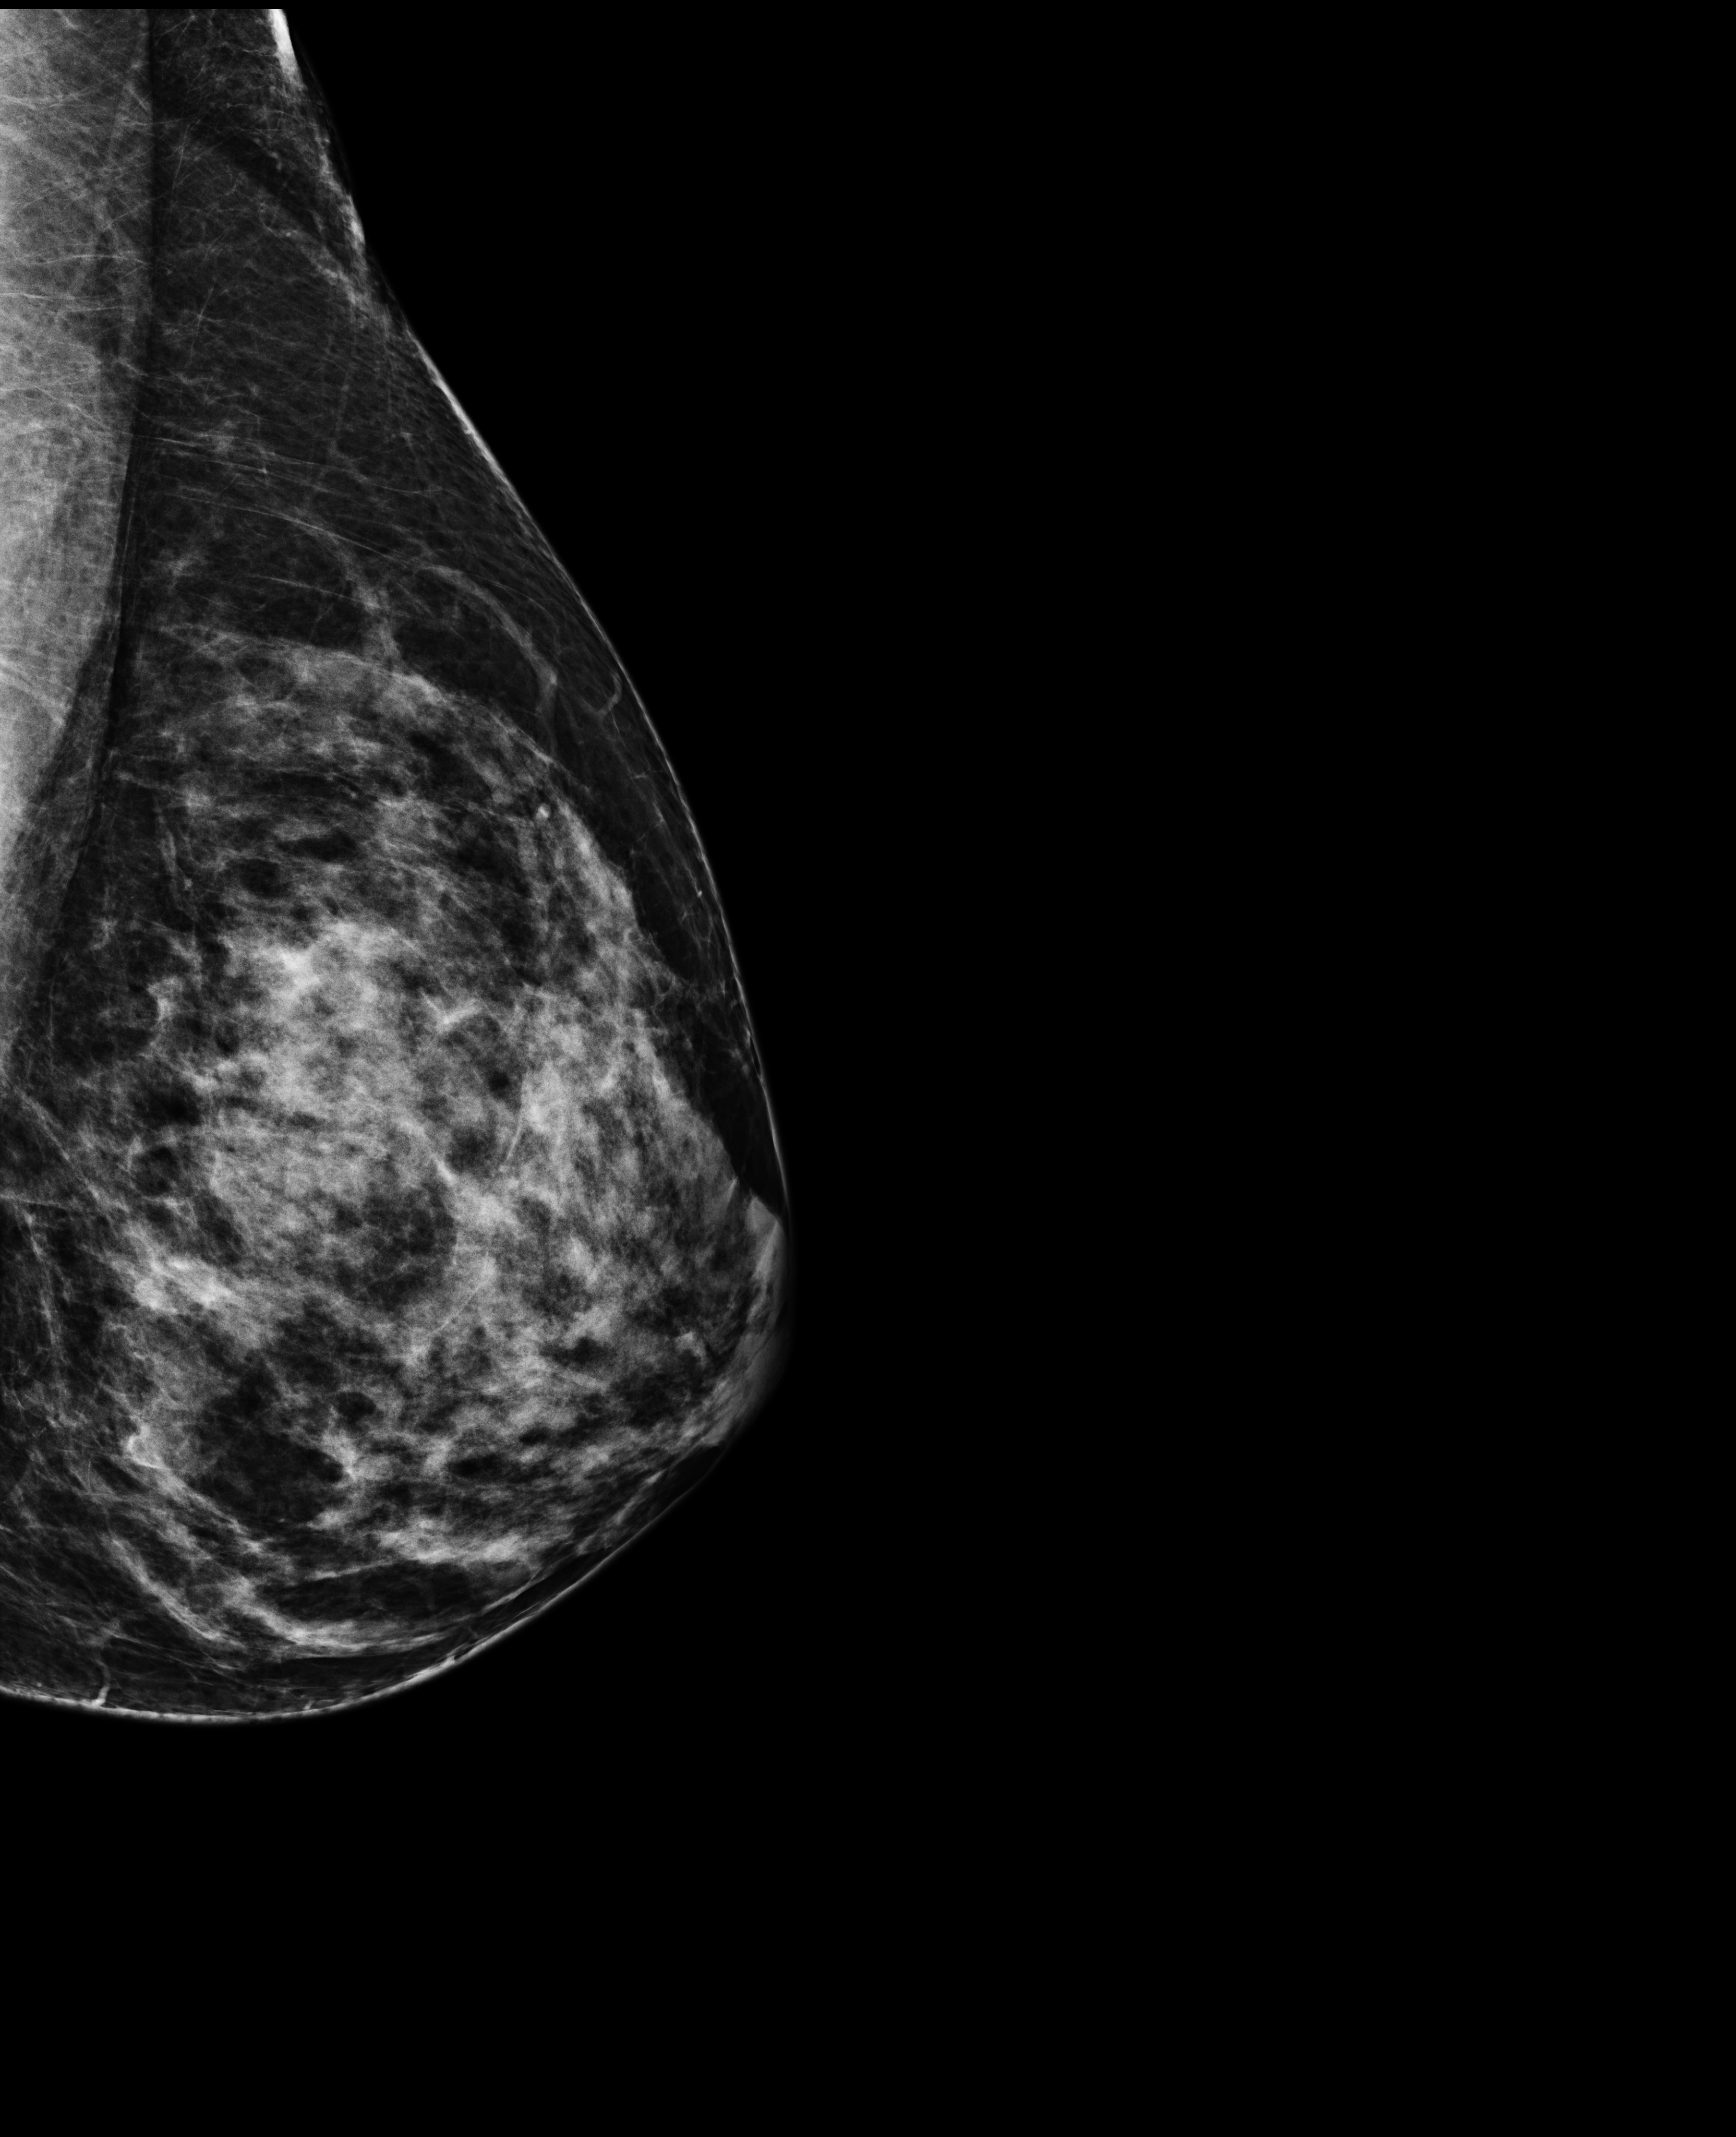
Annual screening mammography examination. Patient aged 43 years (female).
Image type: full-field digital mammogram. Breast: left. Projection: exaggerated CC view (lateral).